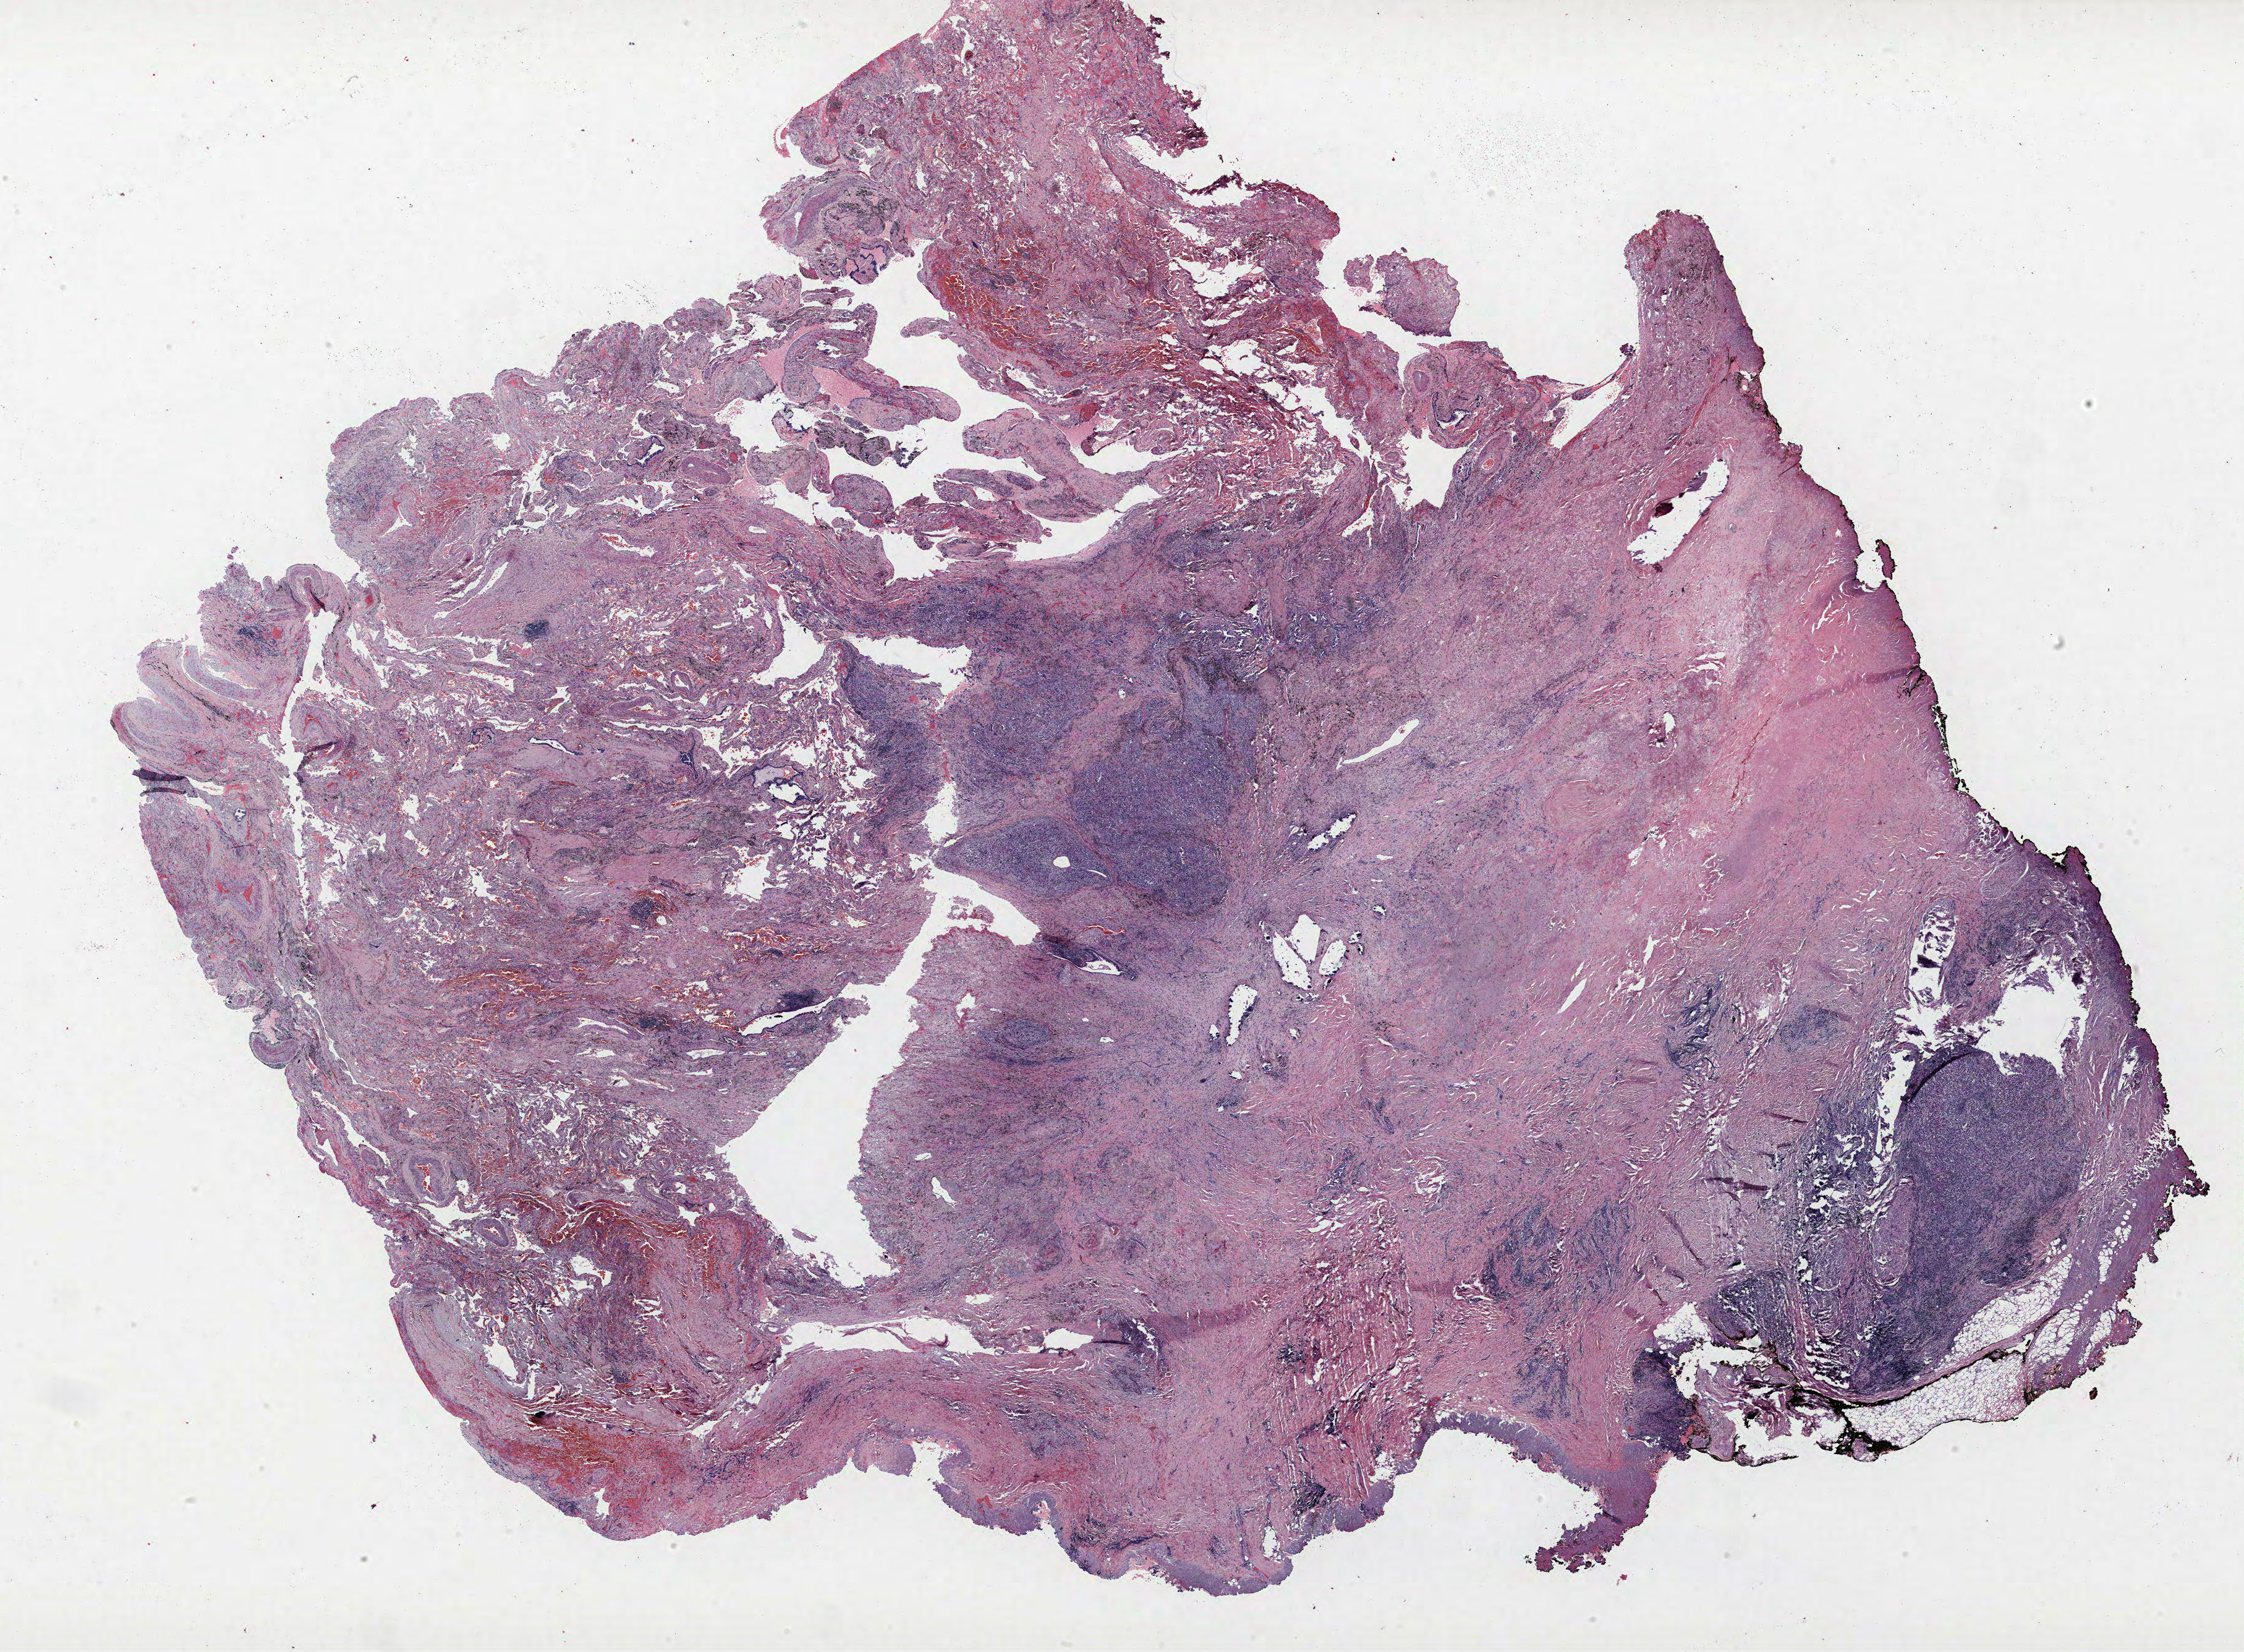
Hematoxylin and eosin (H&E) stained whole-slide image — whole scanned area (about 29.0 x 21.4 mm, from a 40x scan) shown as a low-resolution overview; formalin-fixed paraffin-embedded (FFPE) section; lung tissue. Male, age 65 at enrolment. Grade: poorly differentiated (G3).
Tumour size (pathology): 13 mm. Participant's lung-cancer diagnosis: Adenocarcinoma, NOS (ICD-O-3 8140/3). Primary tumour location (clinical record): right upper lobe. Stage (AJCC 6th edition): IB. Note: participant had 2 primary lung cancers recorded; fields above describe the first.